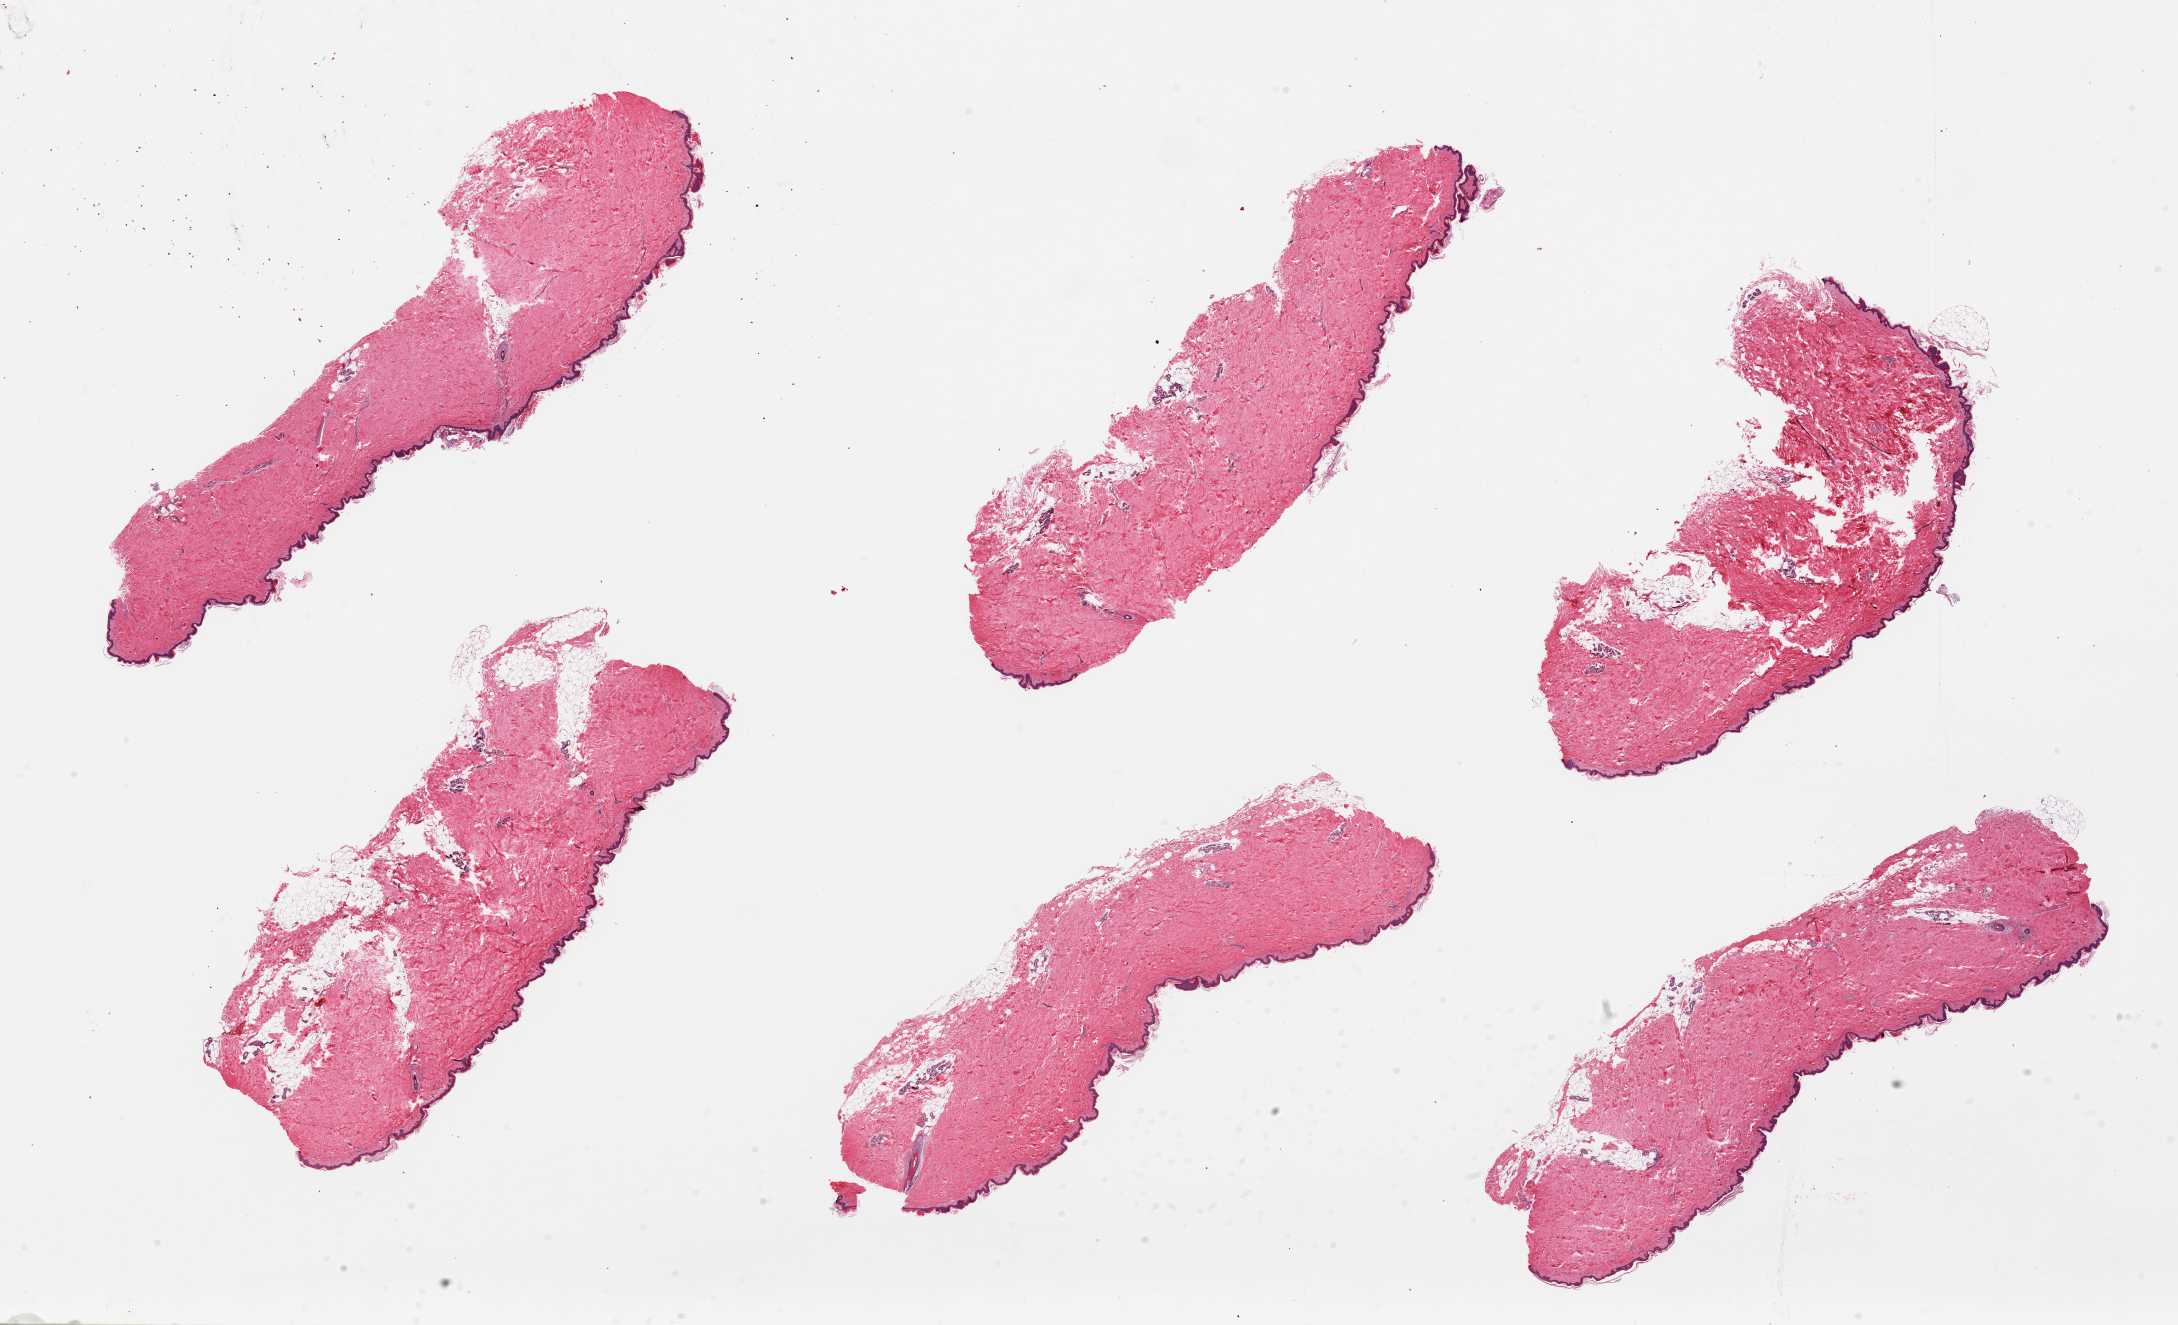
Digitized haematoxylin and eosin-stained section — whole scanned area (about 34.5 x 21.0 mm, slide scanned at 20x) shown as a low-resolution overview. PAXgene-fixed paraffin-embedded (PFPE) section. Section of skin of suprapubic region (target tissue). Donor tissue sample. Donor: female.
Reviewer comment on this tissue sample: 6 pieces, up to 12.5x4mm; squamous epitheium is ~2% thickness.